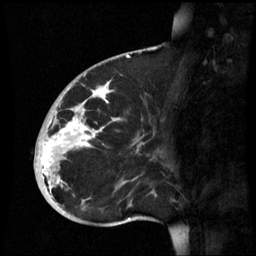
Breast MRI (dynamic contrast-enhanced), one sagittal slice. Dynamic contrast-enhanced series, image 2 of 3 at this slice position (ordered by acquisition). 1.5 T. TE 4.2 ms, TR 8.9 ms. 2.6 mm slice thickness. 256 × 256 image matrix, field of view 220 × 220 mm. Female patient, age 35 years. Case-level facts recorded for this patient, not image findings: setting: breast cancer imaged before/during neoadjuvant chemotherapy; receptor status: HR-positive, HER2-negative.
Outlined on this slice (semi-automatically segmented with operator editing):
- analysis volume of interest (the breast-tissue region the enhancement analysis was run in; not a lesion): box from (x=34, y=74) to (x=164, y=221) px
- tumour enhancement mask (voxels above the 70 % enhancement threshold inside the analysis volume of interest): (x=41, y=82)–(x=117, y=191)